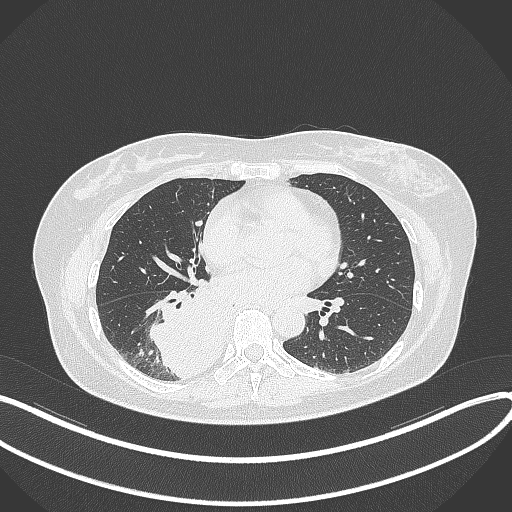
Chest CT, one axial slice; slice 163 of 331 in the series (ordered by position); reconstruction kernel B70f; lung window (W 1500 / L -600 HU); 1 mm slice thickness; 512 × 512 image matrix, field of view 400 × 400 mm. Female patient, age 54 years. Case-level facts recorded for this patient, not image findings: clinical TNM (as recorded): T4 N0 M0.
Outlined on this slice (rectangle marked by the reading radiologist):
- lung tumour (recorded histology: adenocarcinoma): bounding box <150,289,223,378> (left, top, right, bottom; pixels)